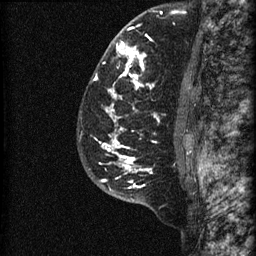
Breast MRI (dynamic contrast-enhanced), one sagittal slice; dynamic contrast-enhanced series, image 2 of 3 at this slice position (ordered by acquisition); 1.5 T; TE 4.2 ms, TR 22.7 ms; 1.5 mm slice thickness; 256 × 256 image matrix, field of view 180 × 180 mm. Patient: female, 48 years. Case-level facts recorded for this patient, not image findings: setting: breast cancer imaged before/during neoadjuvant chemotherapy; receptor status: triple-negative.
Outlined on this slice (semi-automatic segmentation, software-assisted and operator-edited):
- analysis volume of interest (the breast-tissue region the enhancement analysis was run in; not a lesion): box from (x=81, y=23) to (x=186, y=202) px
- tumour enhancement mask (voxels above the 90 % enhancement threshold inside the analysis volume of interest): (x=94, y=25)–(x=160, y=188)